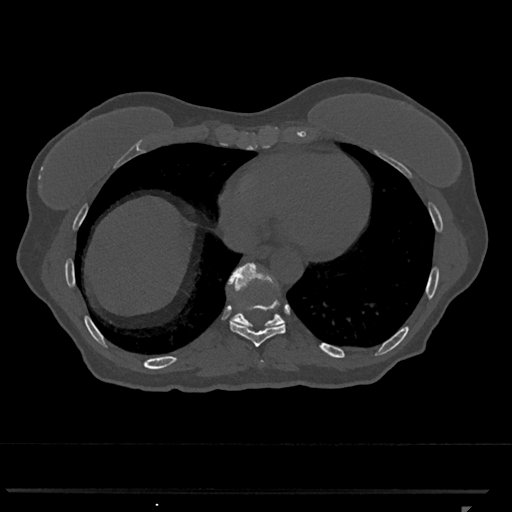
CT including the spine, one axial slice. Slice 605 of 793 in the series (ordered by position). Bone window (W 1800 / L 400 HU). 512 × 512 image matrix, field of view 380 × 380 mm. Patient: female, 62 years. From the clinical record (not read from this slice): primary cancer: renal.
Structures marked on this image (semi-automatically segmented with operator editing):
- T10 vertebra: box from (x=228, y=263) to (x=285, y=327) px
- T9 vertebra: (x=230, y=299)–(x=286, y=347)